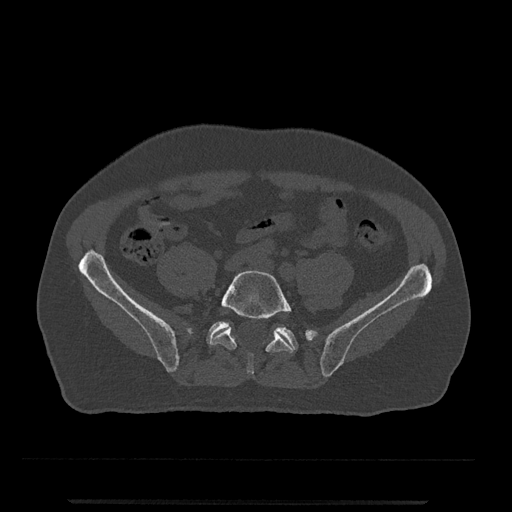
CT including the spine, one axial slice; slice 59 of 797 in the series (ordered by position); reconstruction kernel Br40s/3; bone window (W 1800 / L 400 HU); 0.5 mm slice thickness; 512 × 512 image matrix, field of view 419 × 419 mm. Male patient, age 63 years. Case-level facts recorded for this patient, not image findings: primary cancer: prostate.
Outlined on this slice (semi-automatically segmented with operator editing):
- L5 vertebra: bounding box (x1, y1, x2, y2) in pixels: (210, 270, 293, 375)